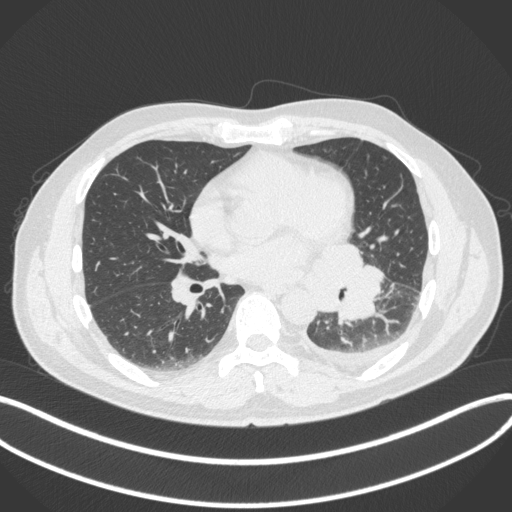
Chest CT, one axial slice. Position 167 of 350 along the scan axis. Lung window (W 1500 / L -600 HU). 512 × 512 image matrix, field of view 400 × 400 mm. Male patient, age 58 years. From the clinical record (not read from this slice): clinical TNM (as recorded): T3 N1 M1b.
Outlined on this slice (rectangle marked by the reading radiologist):
- lung tumour (recorded histology: small cell carcinoma): bounding box (x1, y1, x2, y2) in pixels: (306, 241, 388, 326)